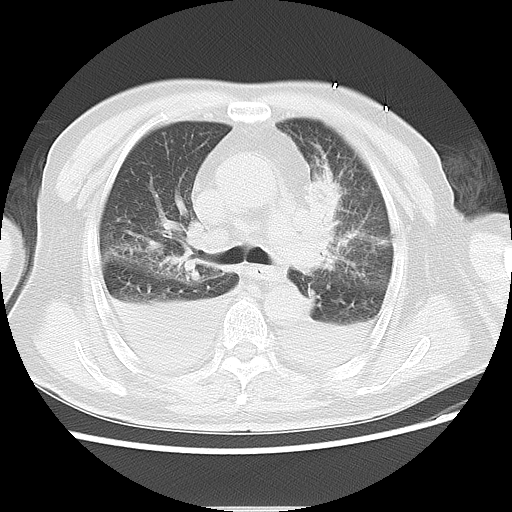
Chest CT, one axial slice; slice 15 of 22 in the series (ordered by position); reconstruction kernel LUNG; 120 kVp; lung window (W 1500 / L -600 HU); 5 mm slice thickness; 512 × 512 image matrix, field of view 350 × 350 mm. Male patient, age 66 years. From the clinical record (not read from this slice): clinical TNM (as recorded): T1c N0 M0.
Outlined on this slice (bounding box drawn by a radiologist):
- lung tumour (recorded histology: adenocarcinoma): box from (x=309, y=173) to (x=343, y=245) px